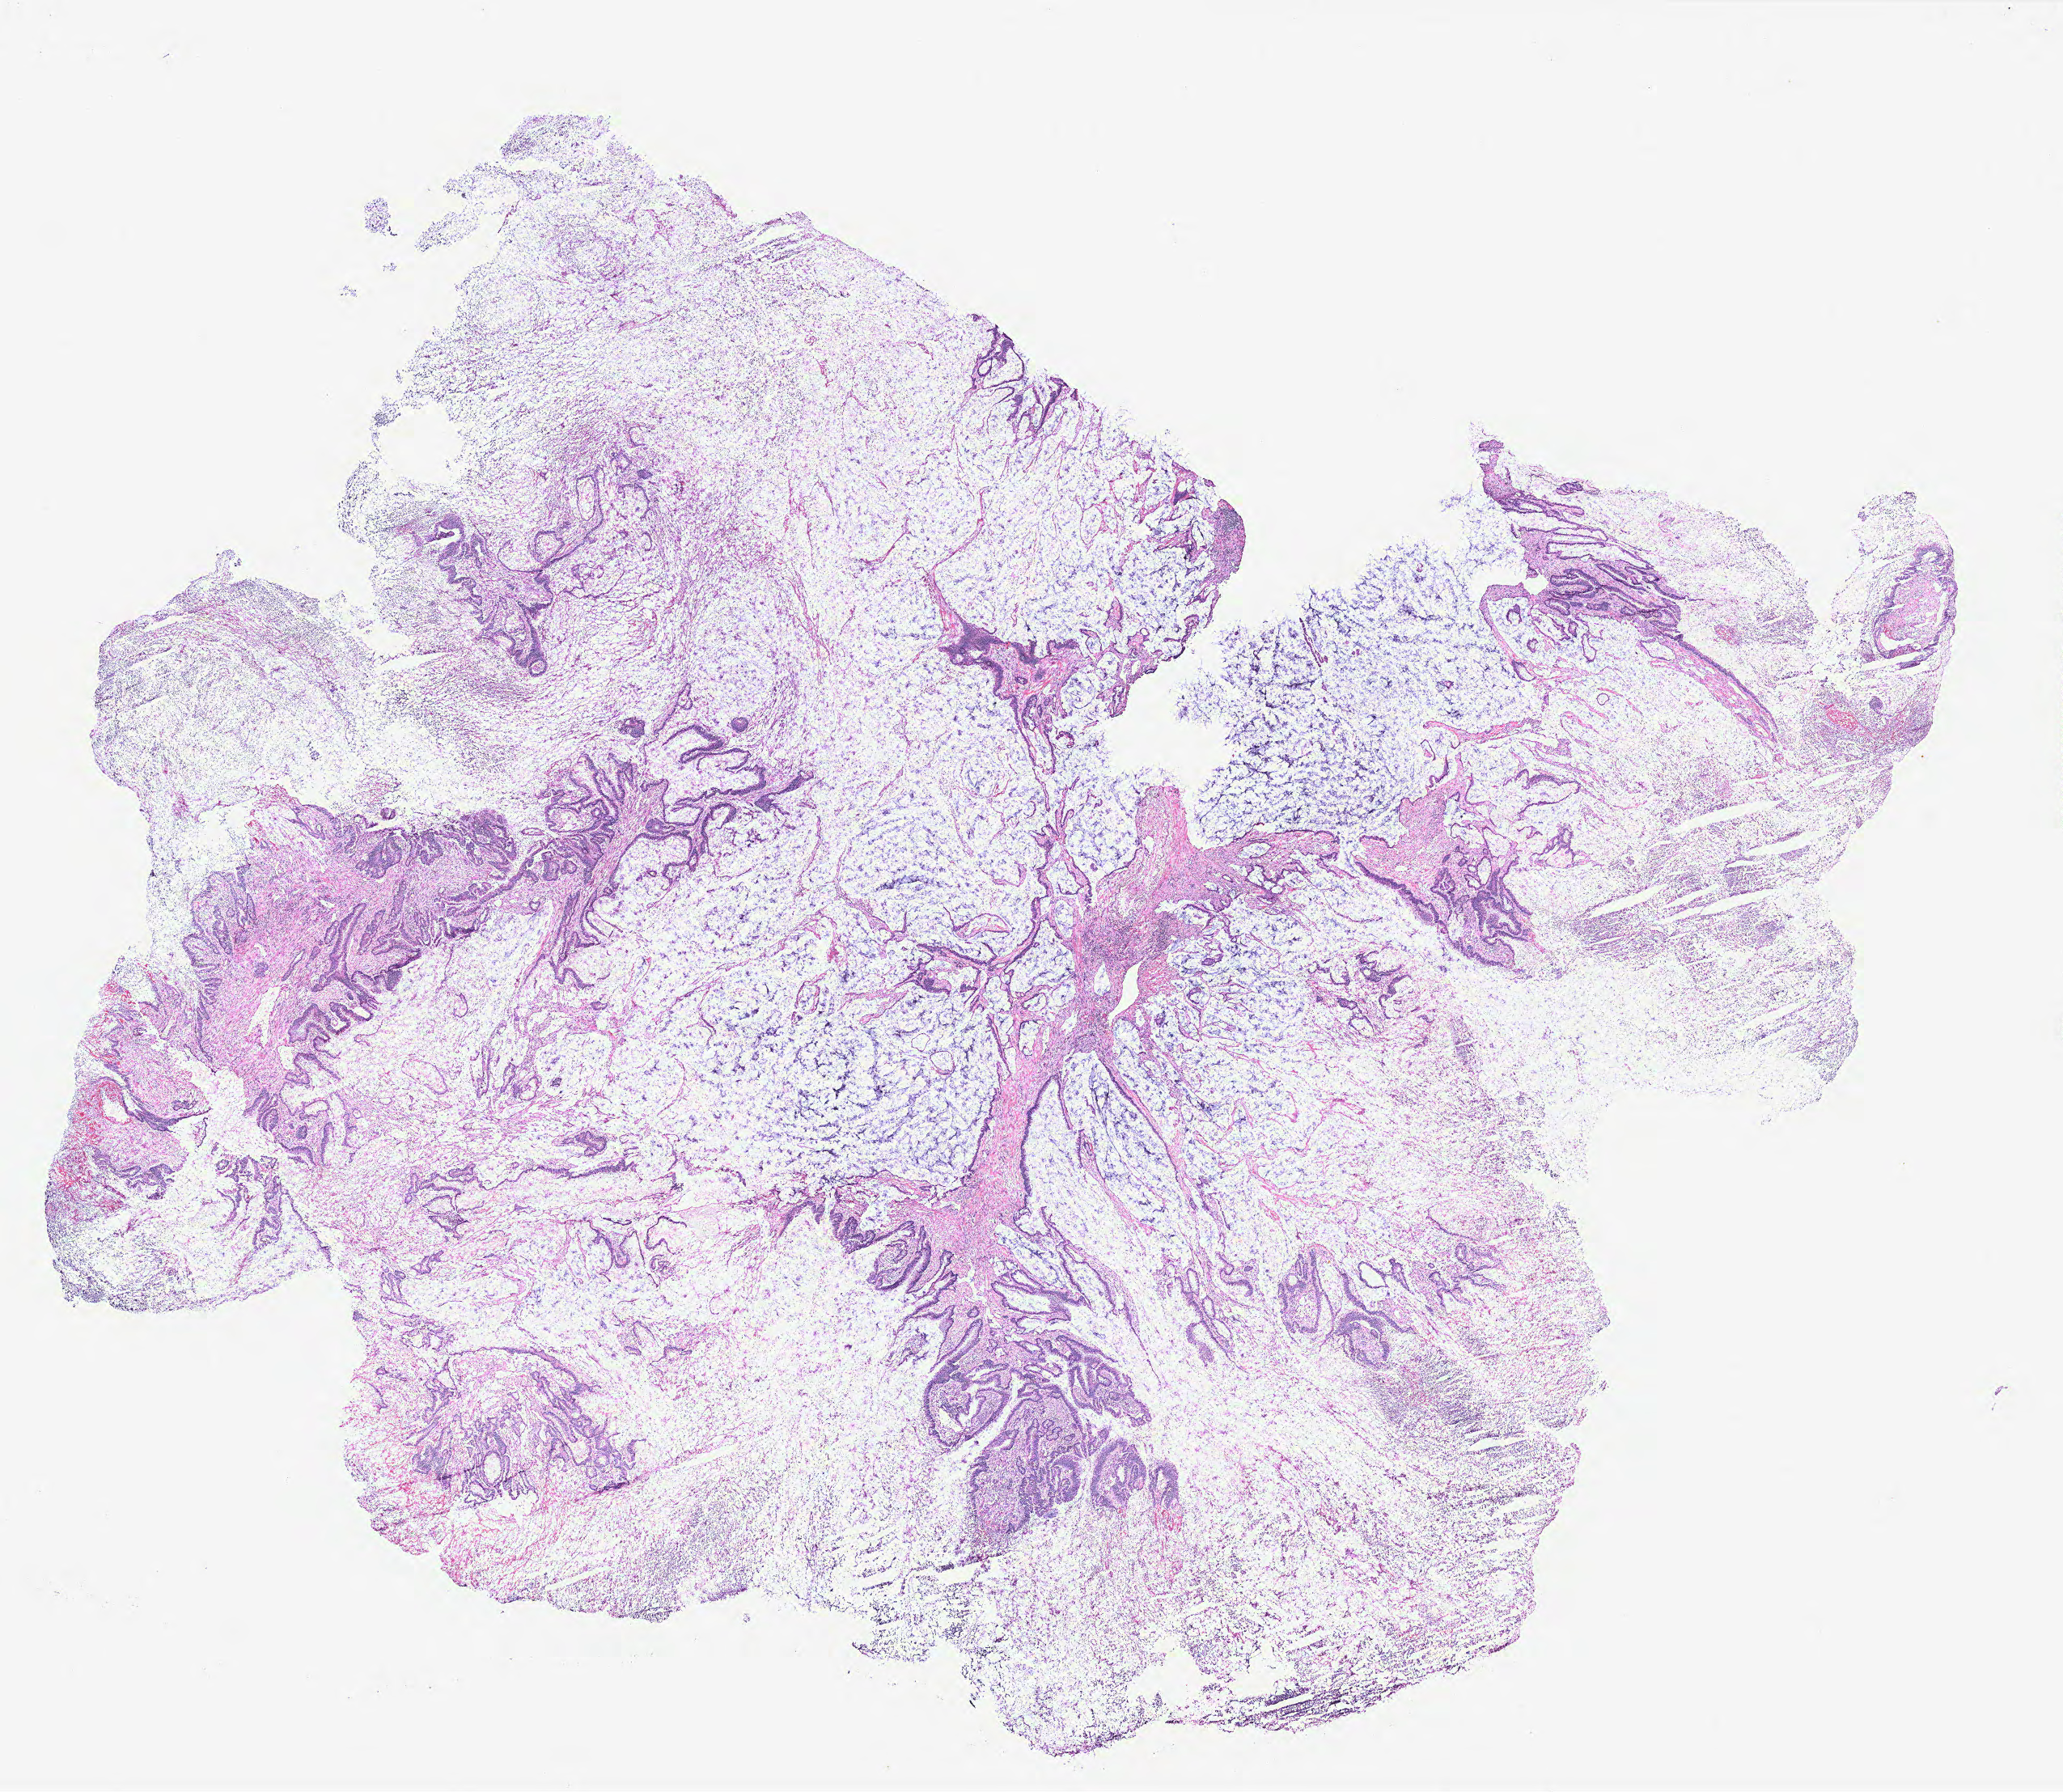
Hematoxylin and eosin (H&E) stained whole-slide image, a low-resolution overview of the entire scanned area, about 20.4 x 17.7 mm (slide scanned at 40x); colon, tissue type not recorded.
- patient diagnosis (cohort enrolment): colon cancer (colon)